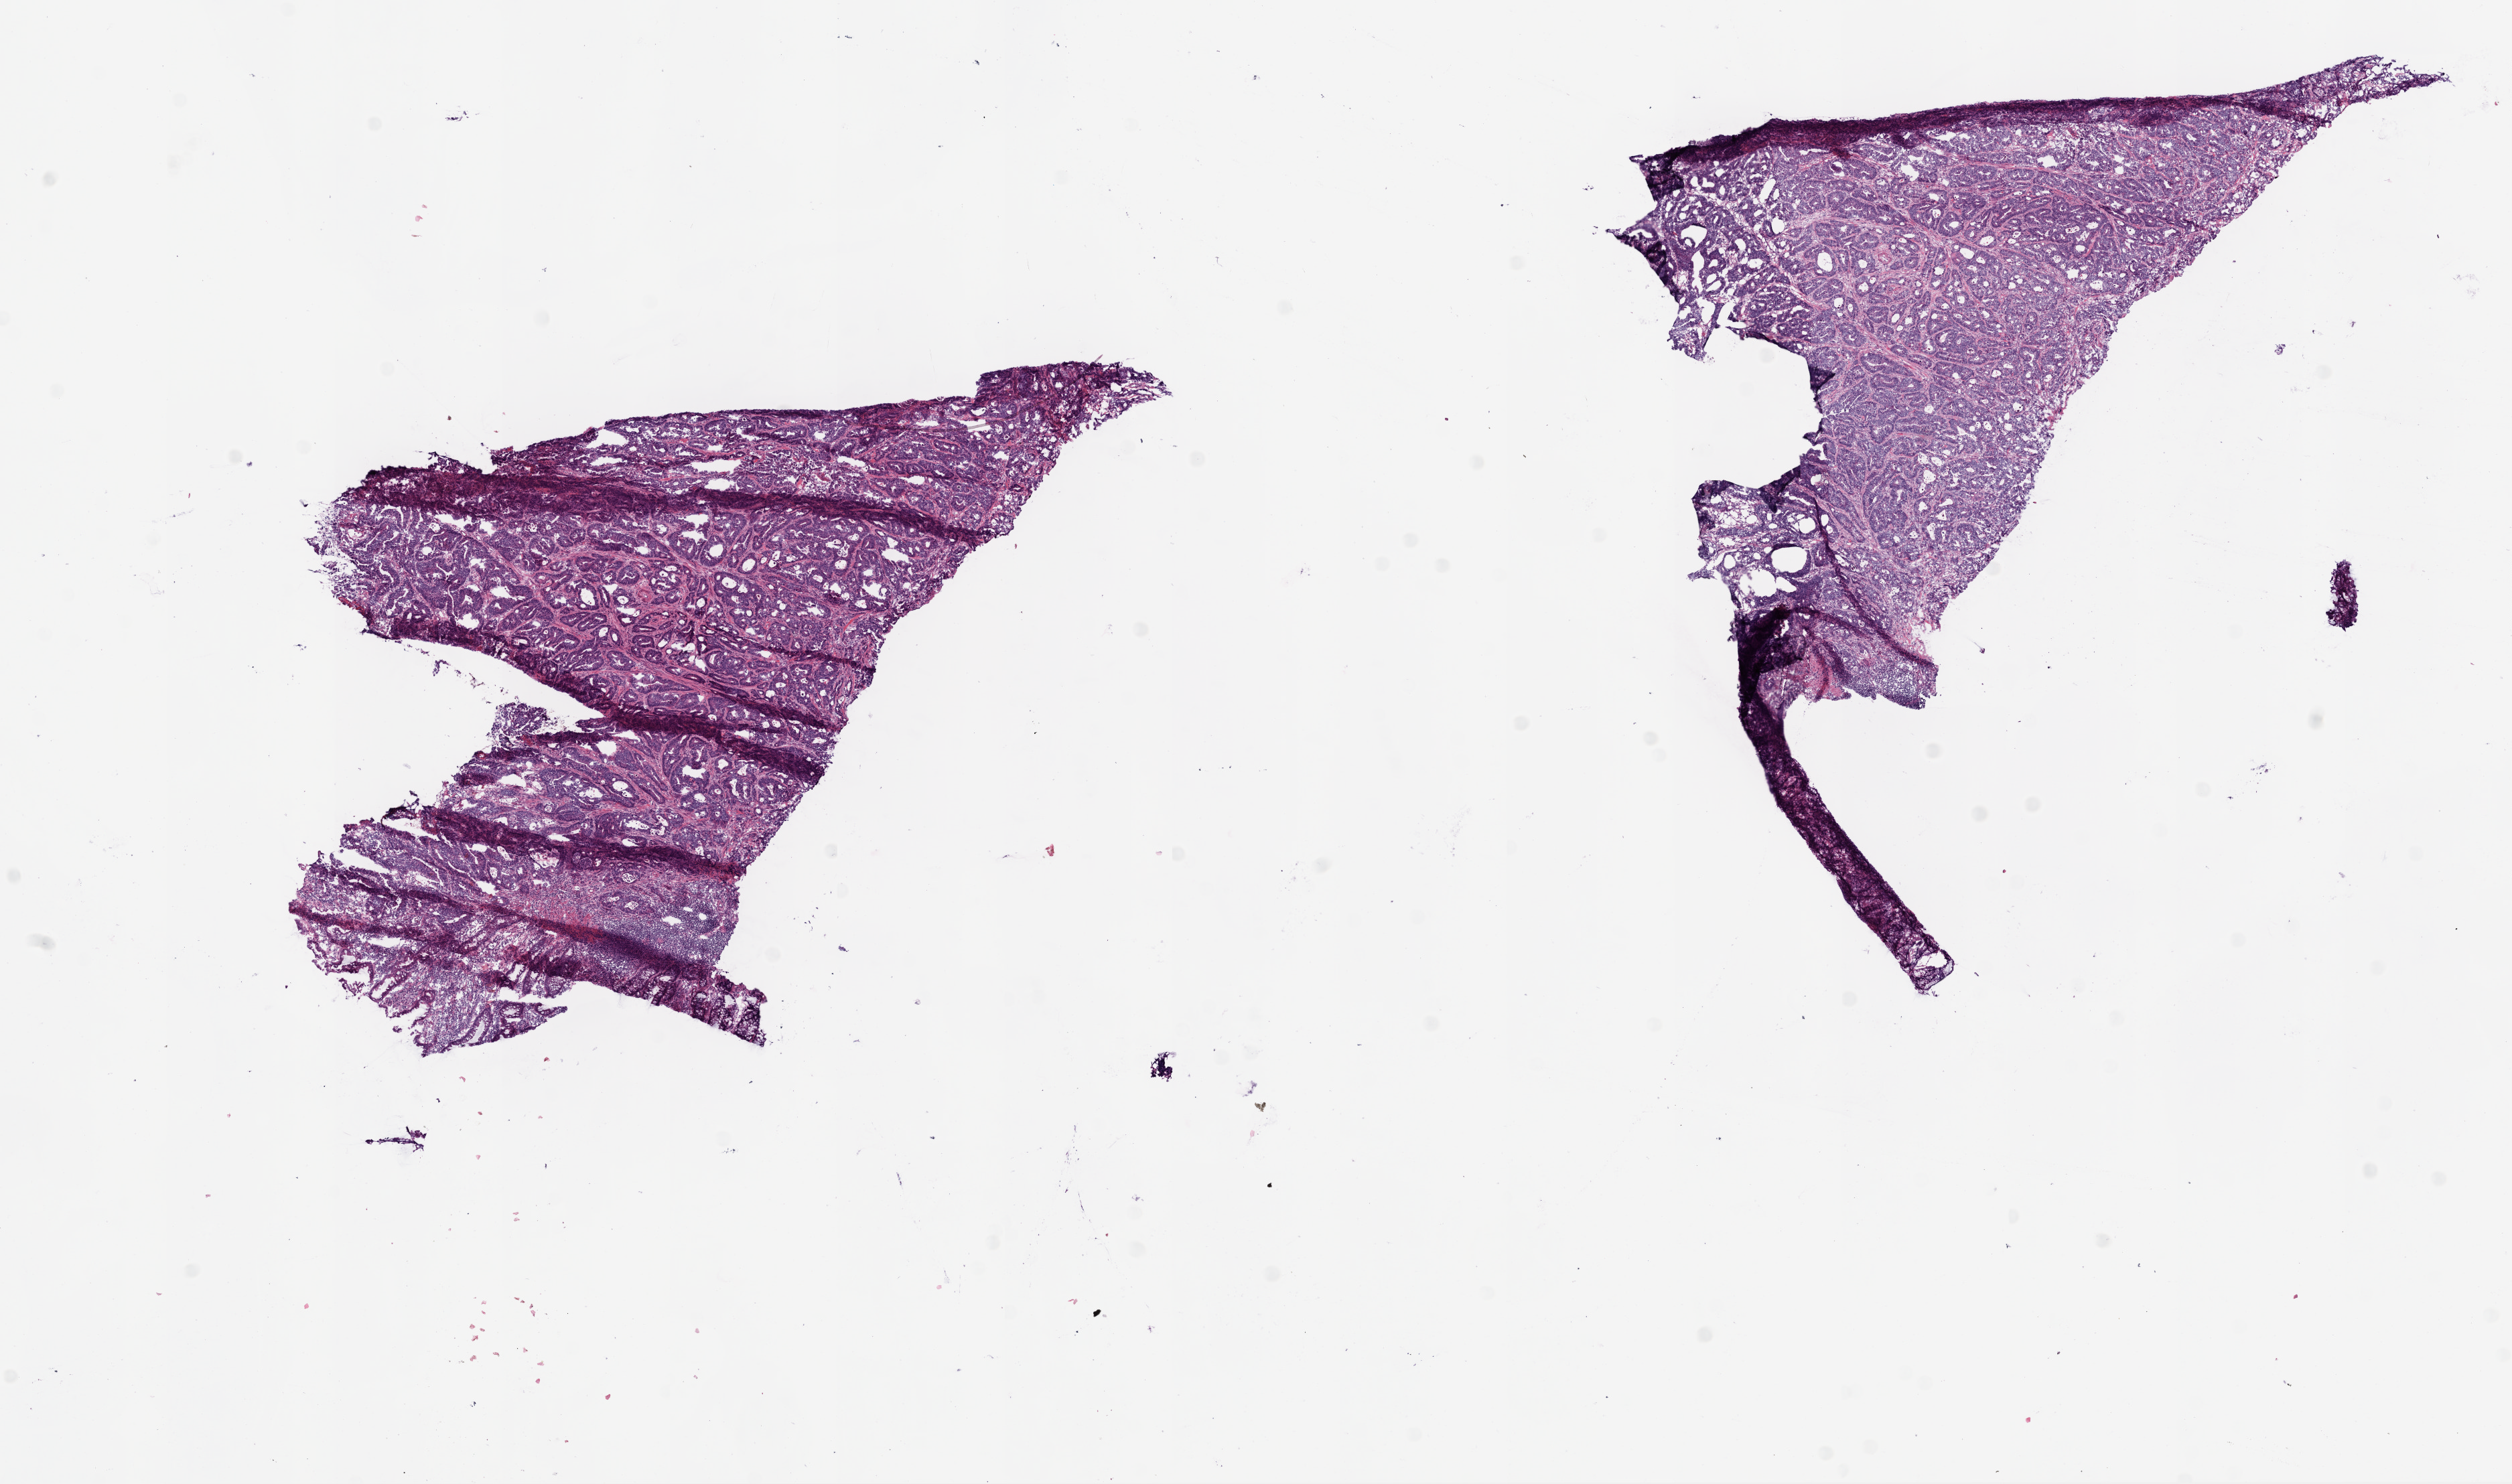
Whole-slide histology image, H&E-stained, a low-resolution overview of the entire scanned area, about 15.0 x 8.9 mm (from a 20x scan), frozen section from the bottom of the tissue portion, colon, primary tumour sample. Patient: male, age at initial diagnosis 69 years. Pathologist review of this section (percent, as recorded): tumour cells 78%, tumour nuclei 85%, normal cells 2%, stromal cells 20%, necrosis 0%.
* histologic diagnosis: Adenocarcinoma, NOS
* AJCC pathologic stage: I
* lymph nodes positive (case pathology): 0 of 31 examined
* TNM: T2 N0 M0